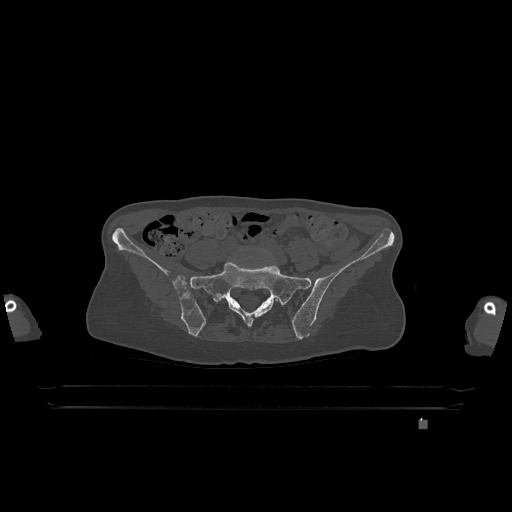
CT including the spine, one axial slice. Position 195 of 1317 along the scan axis. Bone window (W 1800 / L 400 HU). 512 × 512 image matrix, field of view 500 × 500 mm. Patient: female, 74 years. From the clinical record (not read from this slice): primary cancer: lung.
Annotated regions visible in this slice (semi-automatic segmentation, software-assisted and operator-edited):
- L5 vertebra: bounding box <276,299,278,301> (left, top, right, bottom; pixels)